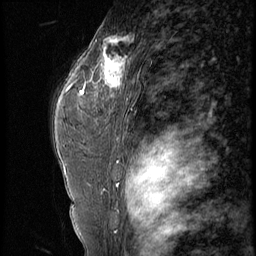
Breast MRI (dynamic contrast-enhanced), one sagittal slice. Position 40 of 56 along the scan axis. 4 images stored at this slice position (order not interpretable as contrast timing). 1.5 T. TE 4.2 ms, TR 9 ms. 256 × 256 image matrix. Female patient, age 44 years. Case-level facts recorded for this patient, not image findings: setting: breast cancer imaged before/during neoadjuvant chemotherapy; receptor status: triple-negative.
Annotated regions visible in this slice (semi-automatically segmented with operator editing):
- analysis volume of interest (the breast-tissue region the enhancement analysis was run in; not a lesion): bounding box [x1, y1, x2, y2] px = [87, 28, 132, 99]
- tumour enhancement mask (voxels above the 140 % enhancement threshold inside the analysis volume of interest): [87, 35, 129, 88]